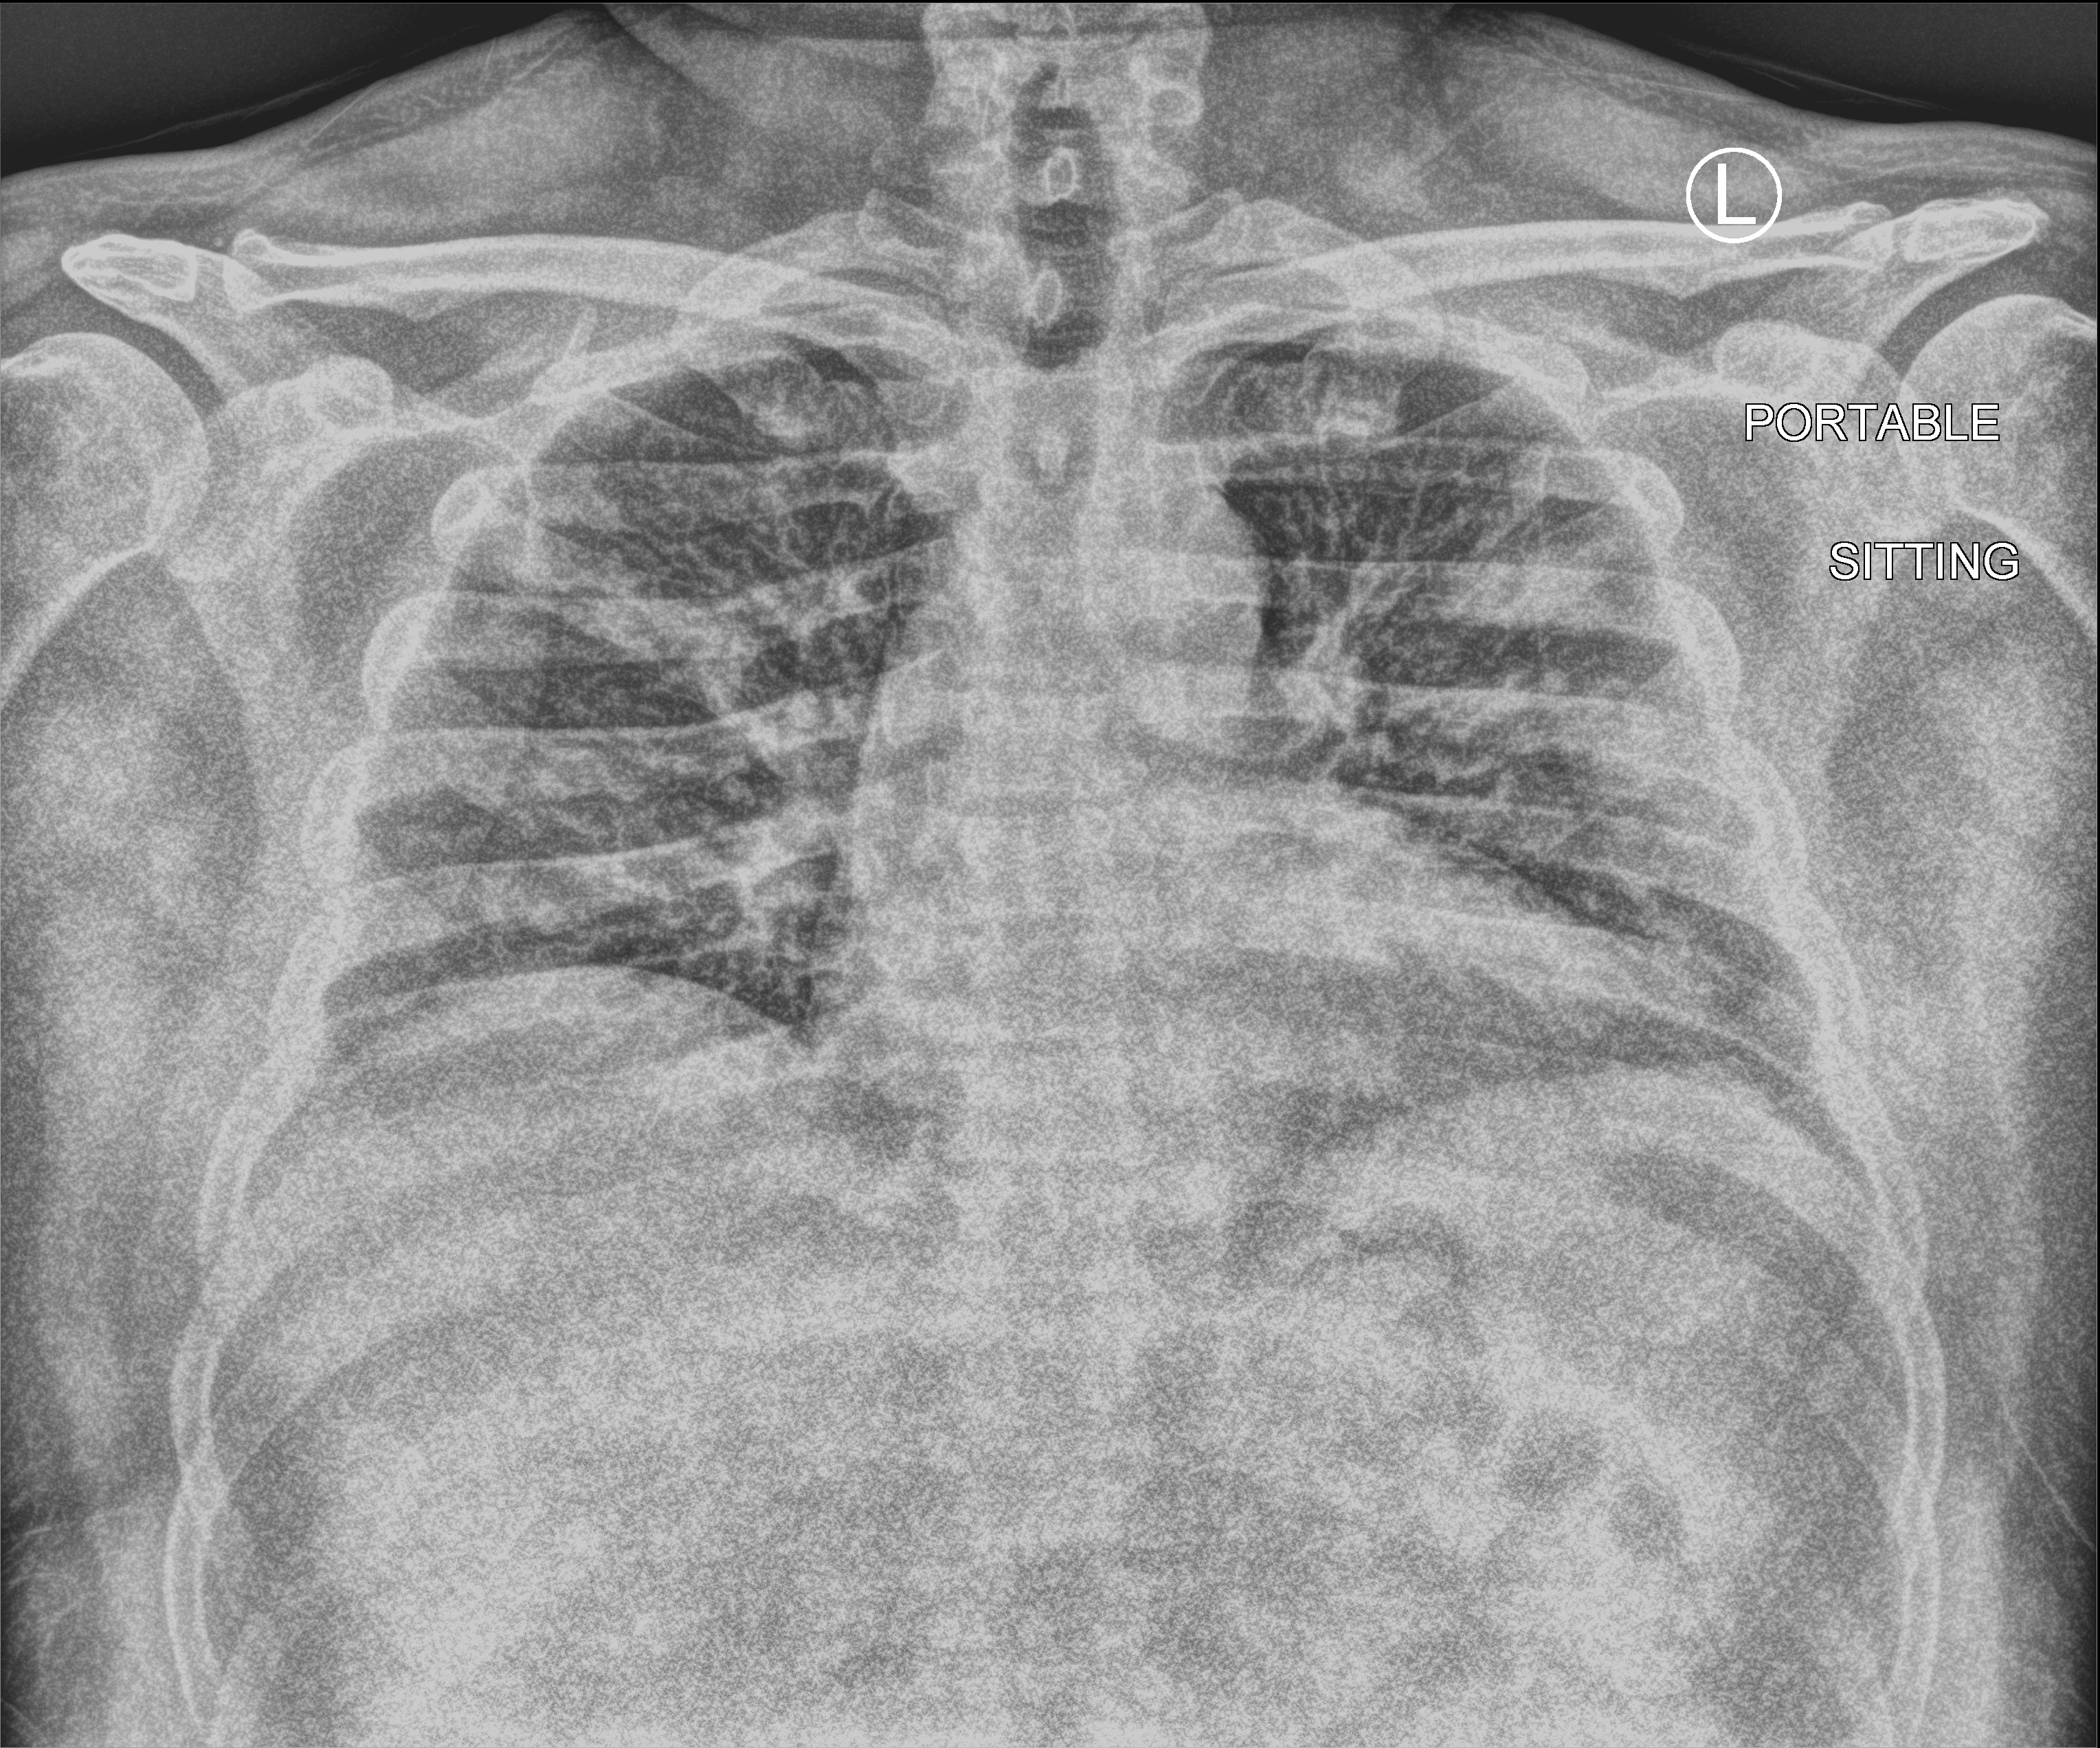
Bedside chest radiograph (computed radiography), anteroposterior (AP) projection. Male patient hospitalised with COVID-19, age 18–59 years.
Hospital-stay facts (about this admission, not read from this image; timing relative to this image not recorded): length of hospital stay: 1 day; mechanically ventilated during this hospital stay: no.